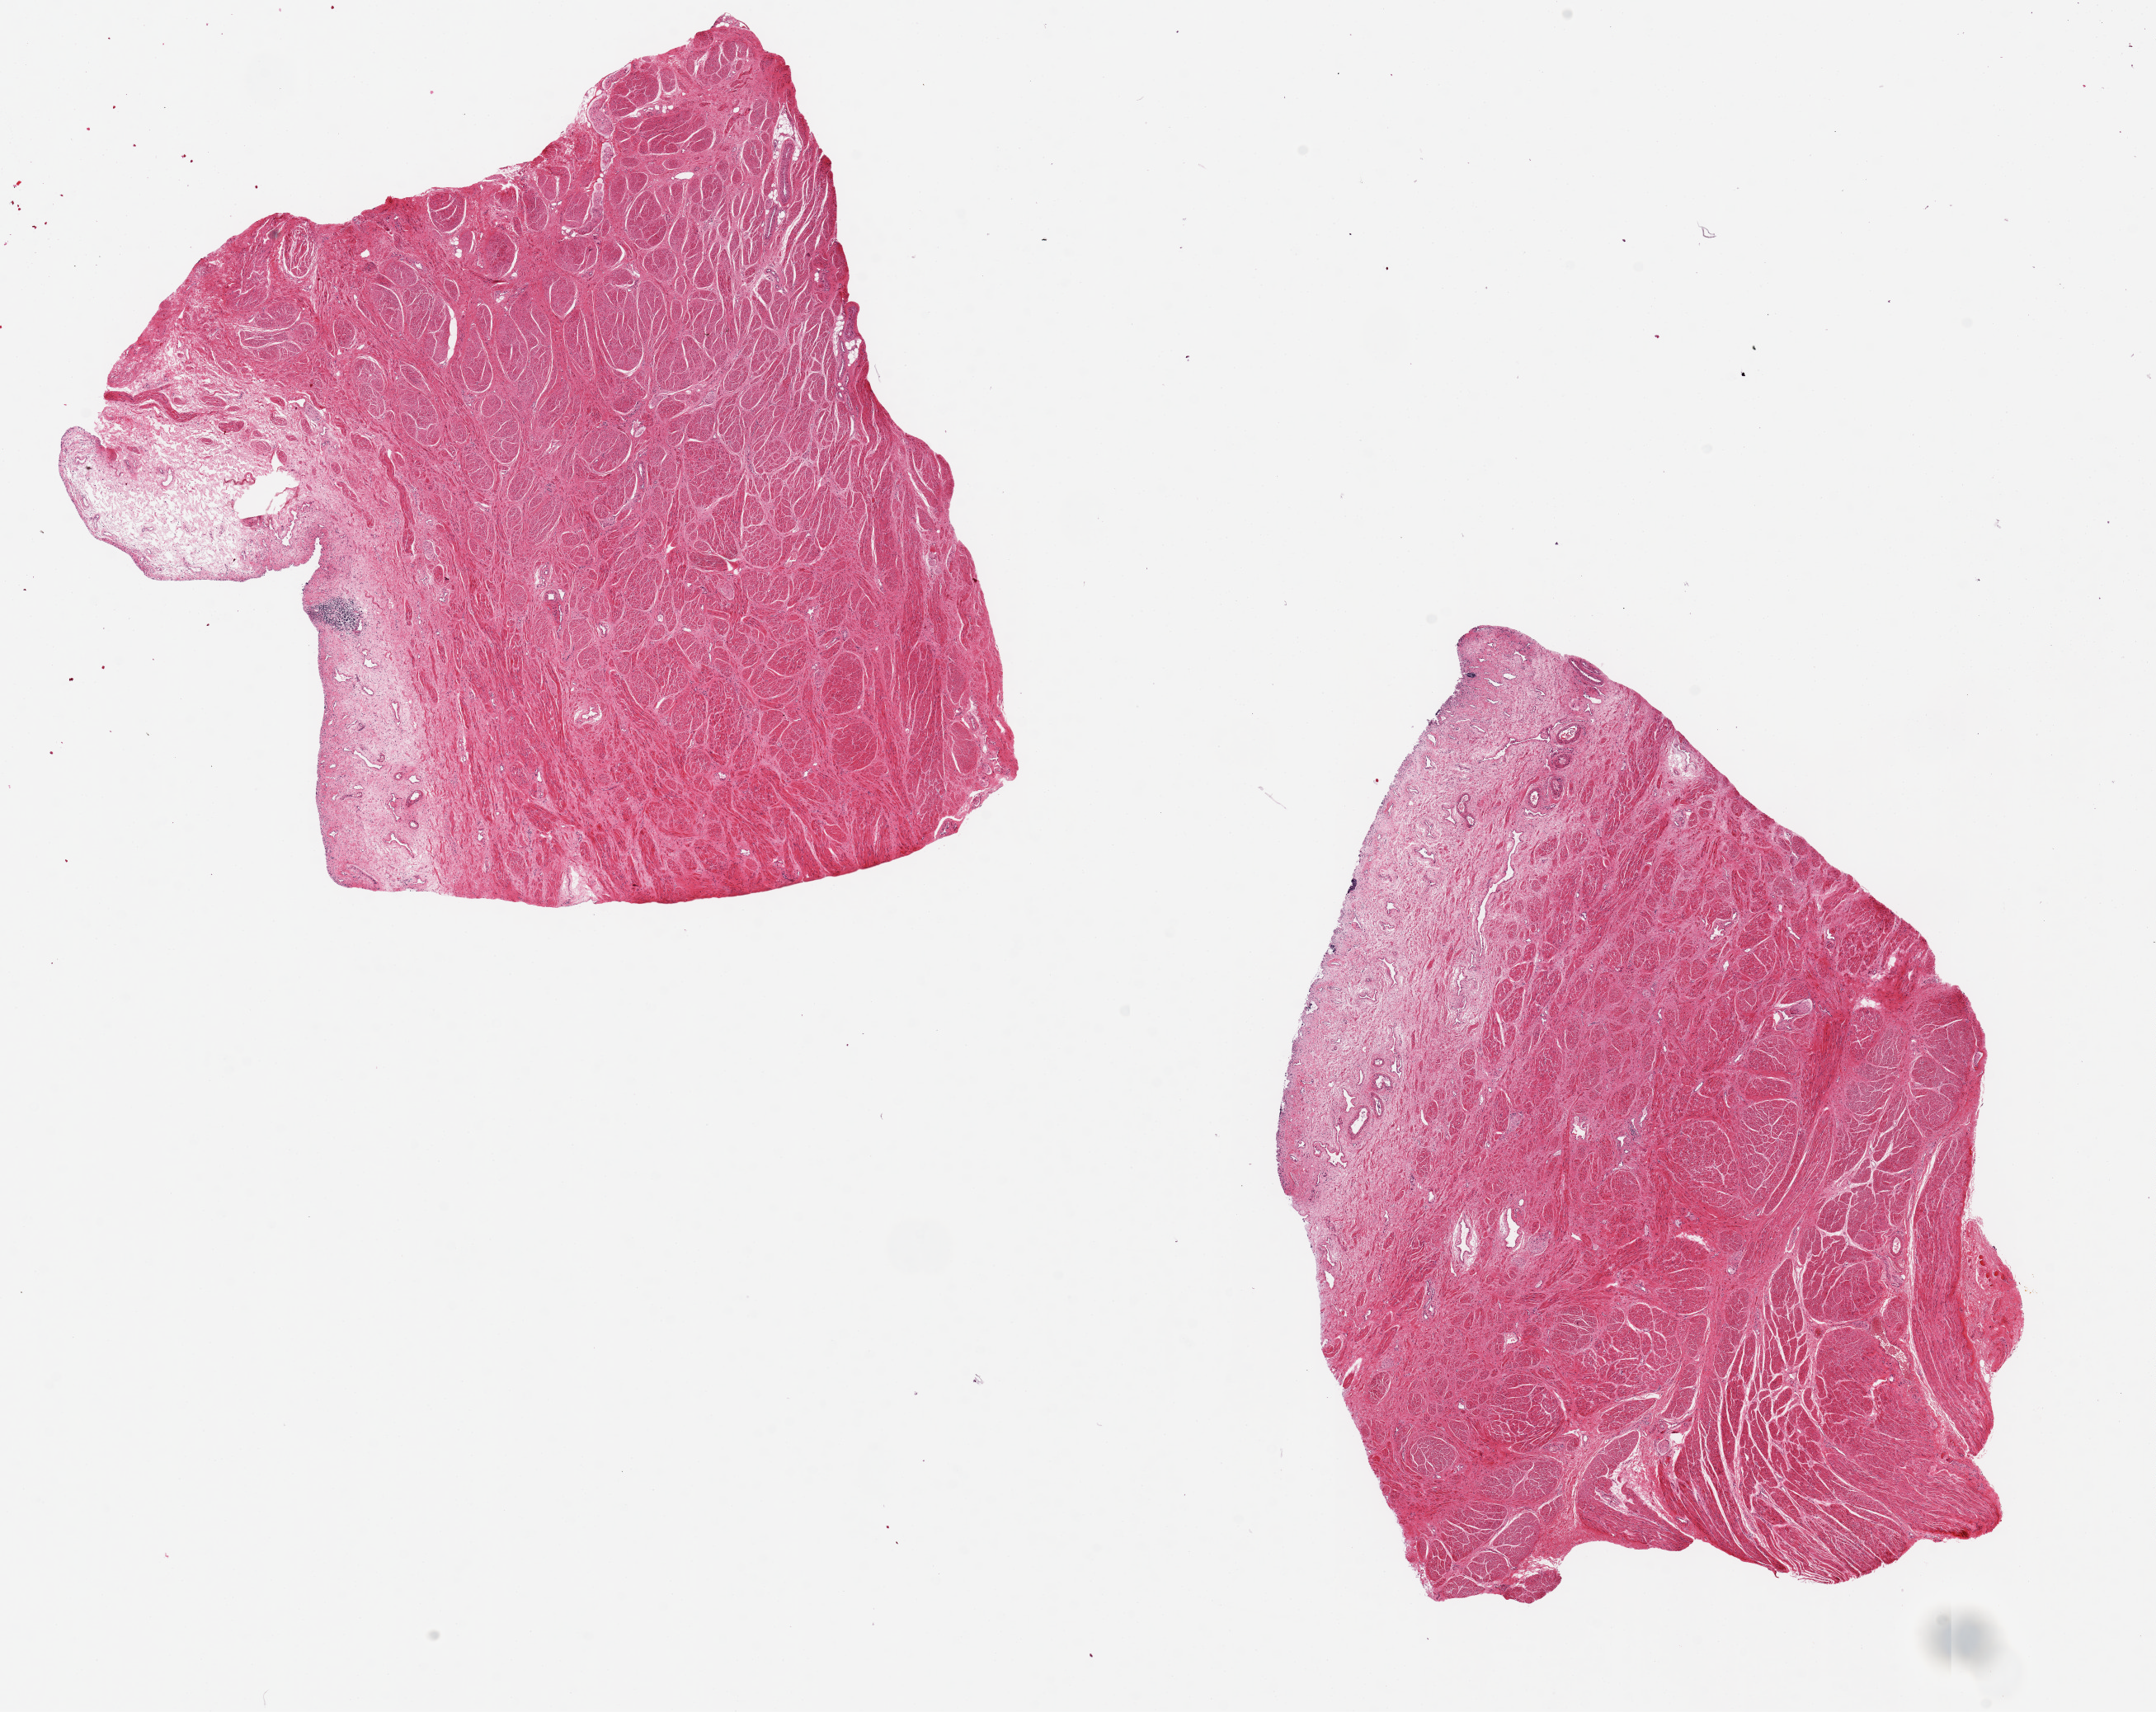
Hematoxylin and eosin (H&E) whole-slide image, a low-resolution overview of the entire scanned area, about 20.7 x 16.4 mm (slide scanned at 20x), PAXgene-fixed, paraffin-embedded tissue, sampled site (target tissue): prostate, tissue donor sample. Male donor.
* reviewer comment on this tissue sample: 2 pieces 9x8 & 8x7 mm; all smooth muscle, no glands